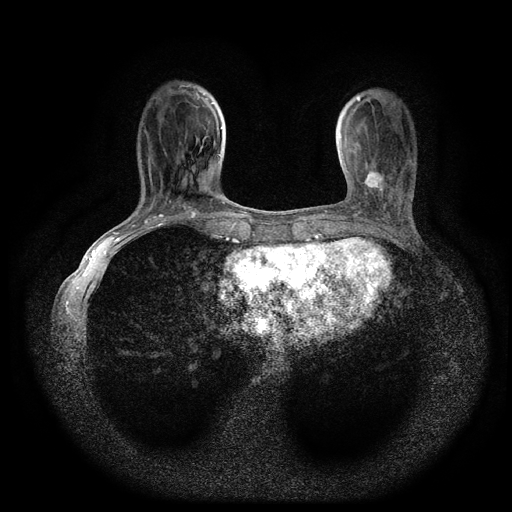
Breast MRI (dynamic contrast-enhanced, multi-phase), one axial slice. Position 29 of 116 along the scan axis. Dynamic contrast-enhanced series, time point 2 of 5 at this slice position (early post-contrast). 1.5 T. TE 2.7 ms, TR 5.4 ms. 2 mm slice thickness. 512 × 512 image matrix, field of view 330 × 330 mm. Female patient, age 49 years.
Annotated regions visible in this slice (semi-automatically segmented with operator editing):
- breast lesion (labelled 'tumour' in the annotation; benign lesions carry a separate 'benign' label): bounding box [x1, y1, x2, y2] px = [361, 168, 385, 193]